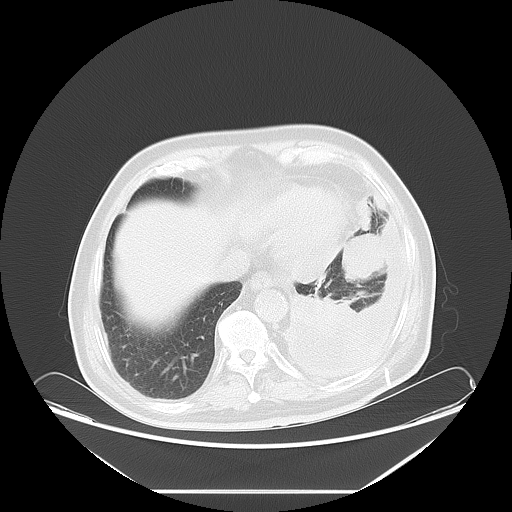
Chest CT, one axial slice; slice 18 of 63 in the series (ordered by position); reconstruction kernel LUNG; 120 kVp; lung window (W 1500 / L -600 HU); 512 × 512 image matrix. Male patient, age 67 years. From the clinical record (not read from this slice): clinical TNM (as recorded): T1b N1 M1a.
Annotated regions visible in this slice (bounding box drawn by a radiologist):
- lung tumour (recorded histology: small cell carcinoma): box from (x=339, y=229) to (x=388, y=284) px